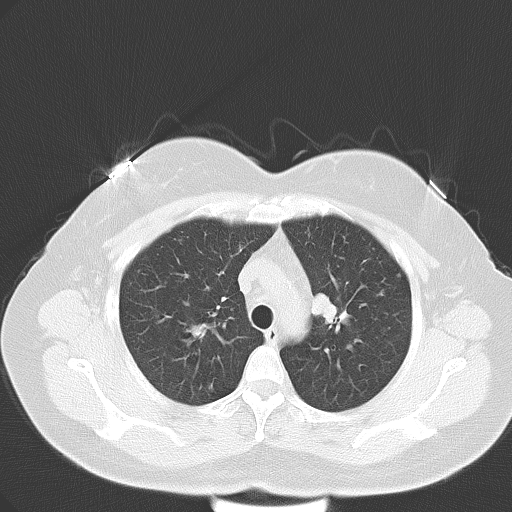
Chest CT, one axial slice. Position 42 of 57 along the scan axis. Reconstruction kernel B70f. Lung window (W 1500 / L -600 HU). 5 mm slice thickness. 512 × 512 image matrix. Patient: female, 53 years. Case-level facts recorded for this patient, not image findings: clinical TNM (as recorded): T1c N0 M1a.
Outlined on this slice (rectangle marked by the reading radiologist):
- lung tumour (recorded histology: adenocarcinoma): bounding box (x1, y1, x2, y2) in pixels: (312, 291, 345, 330)